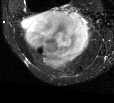
MRI of an extremity soft-tissue mass, one axial slice. Slice 29 of 44 in the series (ordered by position). T2-weighted fat-saturated. MR volume resampled by the dataset authors to the PET/CT grid (not the native acquisition matrix). 3.27 mm slice thickness. 114 × 103 image matrix, field of view 111 × 101 mm. Female patient. From the clinical record (not read from this slice): histological type: liposarcoma; site of the primary tumour: right thigh.
Structures marked on this image (expert contour drawn on MRI and transferred to this co-registered scan by the dataset authors):
- gross tumour volume (mass): bounding box [x1, y1, x2, y2] px = [20, 9, 91, 69]